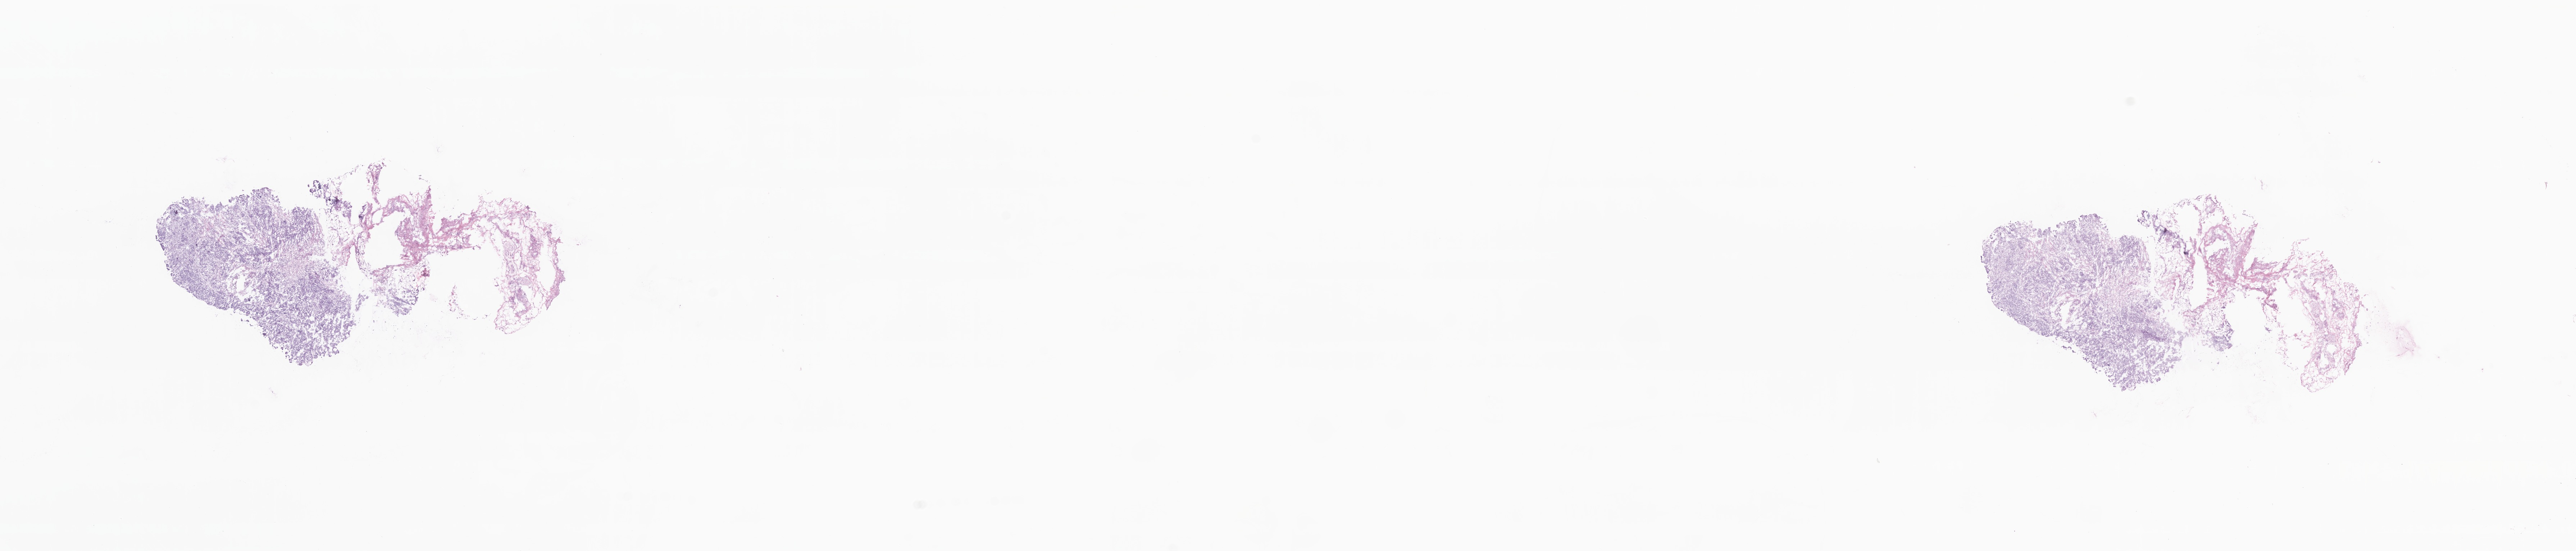
Whole-slide image, H&E stain — low-resolution overview of the scanned area, about 30.2 x 6.5 mm. Cryosection. Metastatic tumor tissue, resected from specified parts of peritoneum. Patient: female, age at initial diagnosis 62 years. Slide review estimates, as recorded: tumor cells 60%, tumor nuclei 50%, stromal cells 5%, necrosis 0%, normal cells 35%. Inflammatory infiltration, as recorded: lymphocyte infiltration 4%, monocyte infiltration 0%, neutrophil infiltration 0%.
- section: top of the tissue portion
- patient diagnosis (primary): High grade serous carcinoma